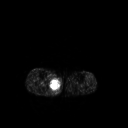
FDG PET of an extremity soft-tissue mass (from a PET/CT study), one axial slice. Slice 143 of 267 in the series (ordered by position). 128 × 128 image matrix, field of view 500 × 500 mm. Patient: male, 69 years. From the clinical record (not read from this slice): histological type: pleiomorphic liposarcoma; grade: high; site of the primary tumour: right calf.
Outlined on this slice (expert contour drawn on MRI and transferred to this co-registered scan by the dataset authors):
- gross tumour volume including surrounding oedema: bounding box <49,77,61,90> (left, top, right, bottom; pixels)
- gross tumour volume (mass): <51,79,61,89>